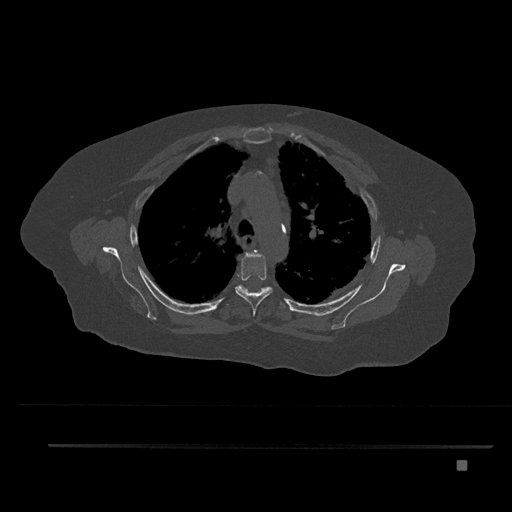
CT including the spine, one axial slice. Position 598 of 797 along the scan axis. Reconstruction kernel Br40s/3. 120 kVp. Bone window (W 1800 / L 400 HU). 512 × 512 image matrix, field of view 437 × 437 mm. Female patient, age 76 years. Case-level facts recorded for this patient, not image findings: primary cancer: lung.
Structures marked on this image (semi-automatically segmented with operator editing):
- T3 vertebra: box from (x=244, y=250) to (x=258, y=258) px
- T4 vertebra: (x=235, y=250)–(x=272, y=316)
- T5 vertebra: (x=237, y=284)–(x=282, y=305)